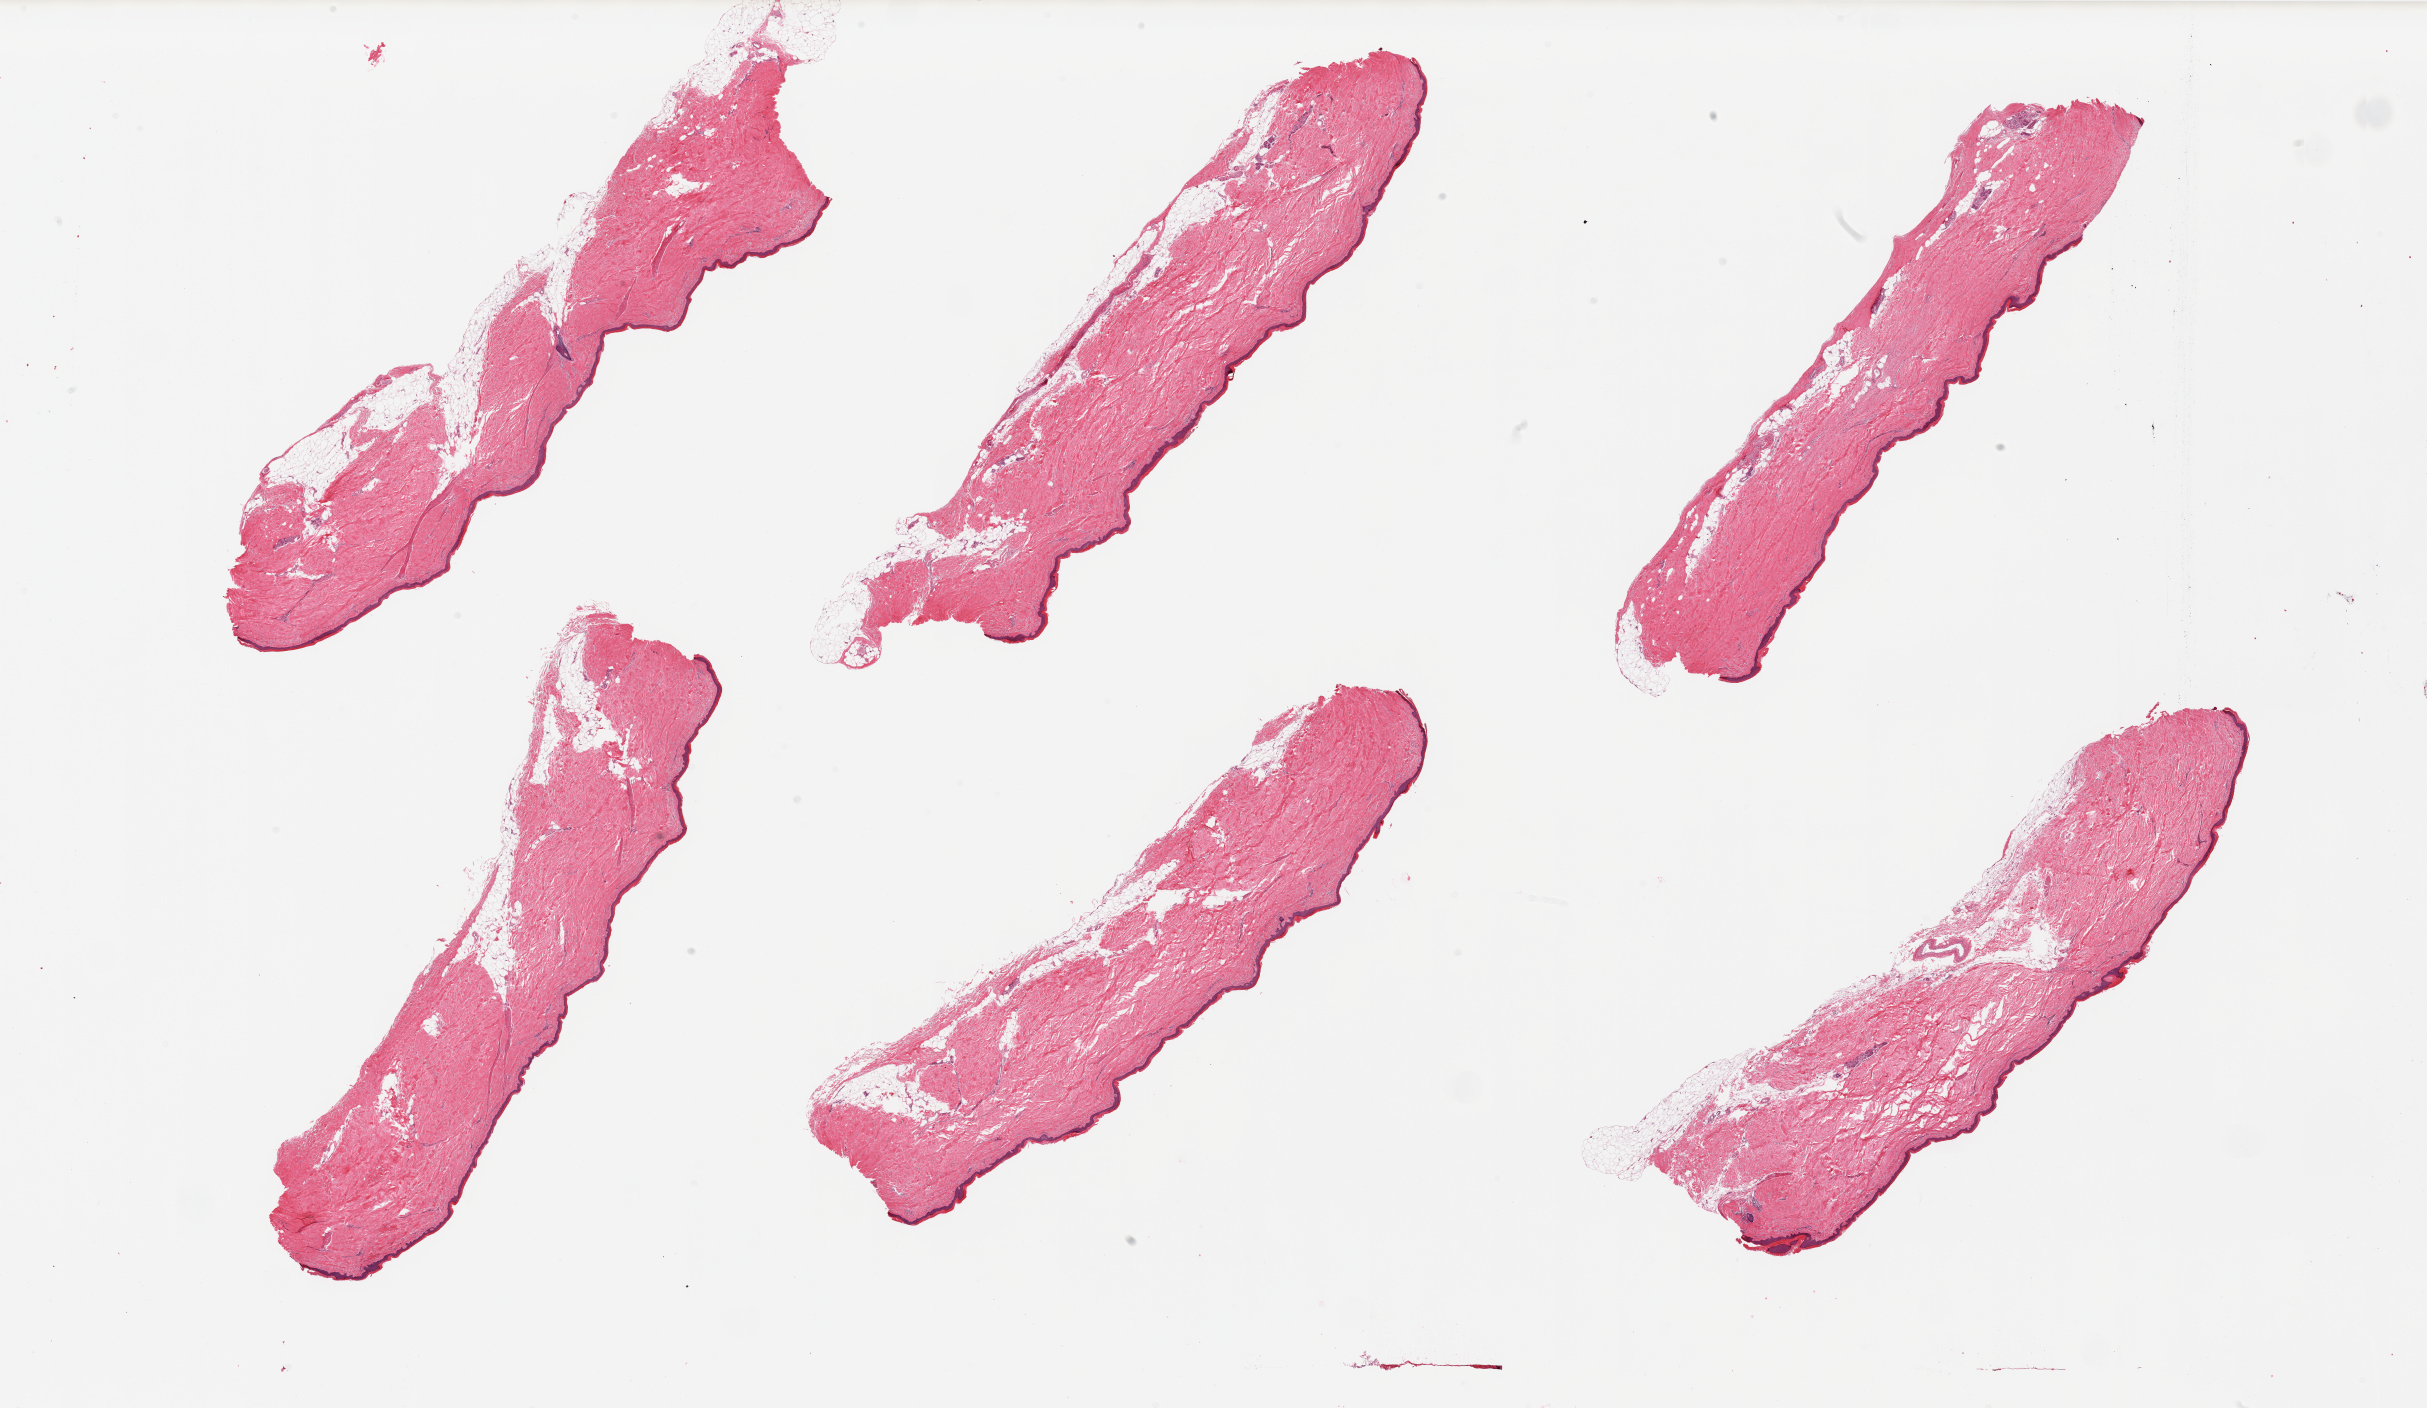
Whole-slide image, H&E stain, whole scanned area (about 38.4 x 22.3 mm) shown as a low-resolution overview, PAXgene-fixed, paraffin-embedded tissue, sampled site (target tissue): skin of lower leg, tissue donor sample. Donor sex: male.
Pathologist's review note for this sample: 2 pieces; well trimmed; 10% intradermal fat.